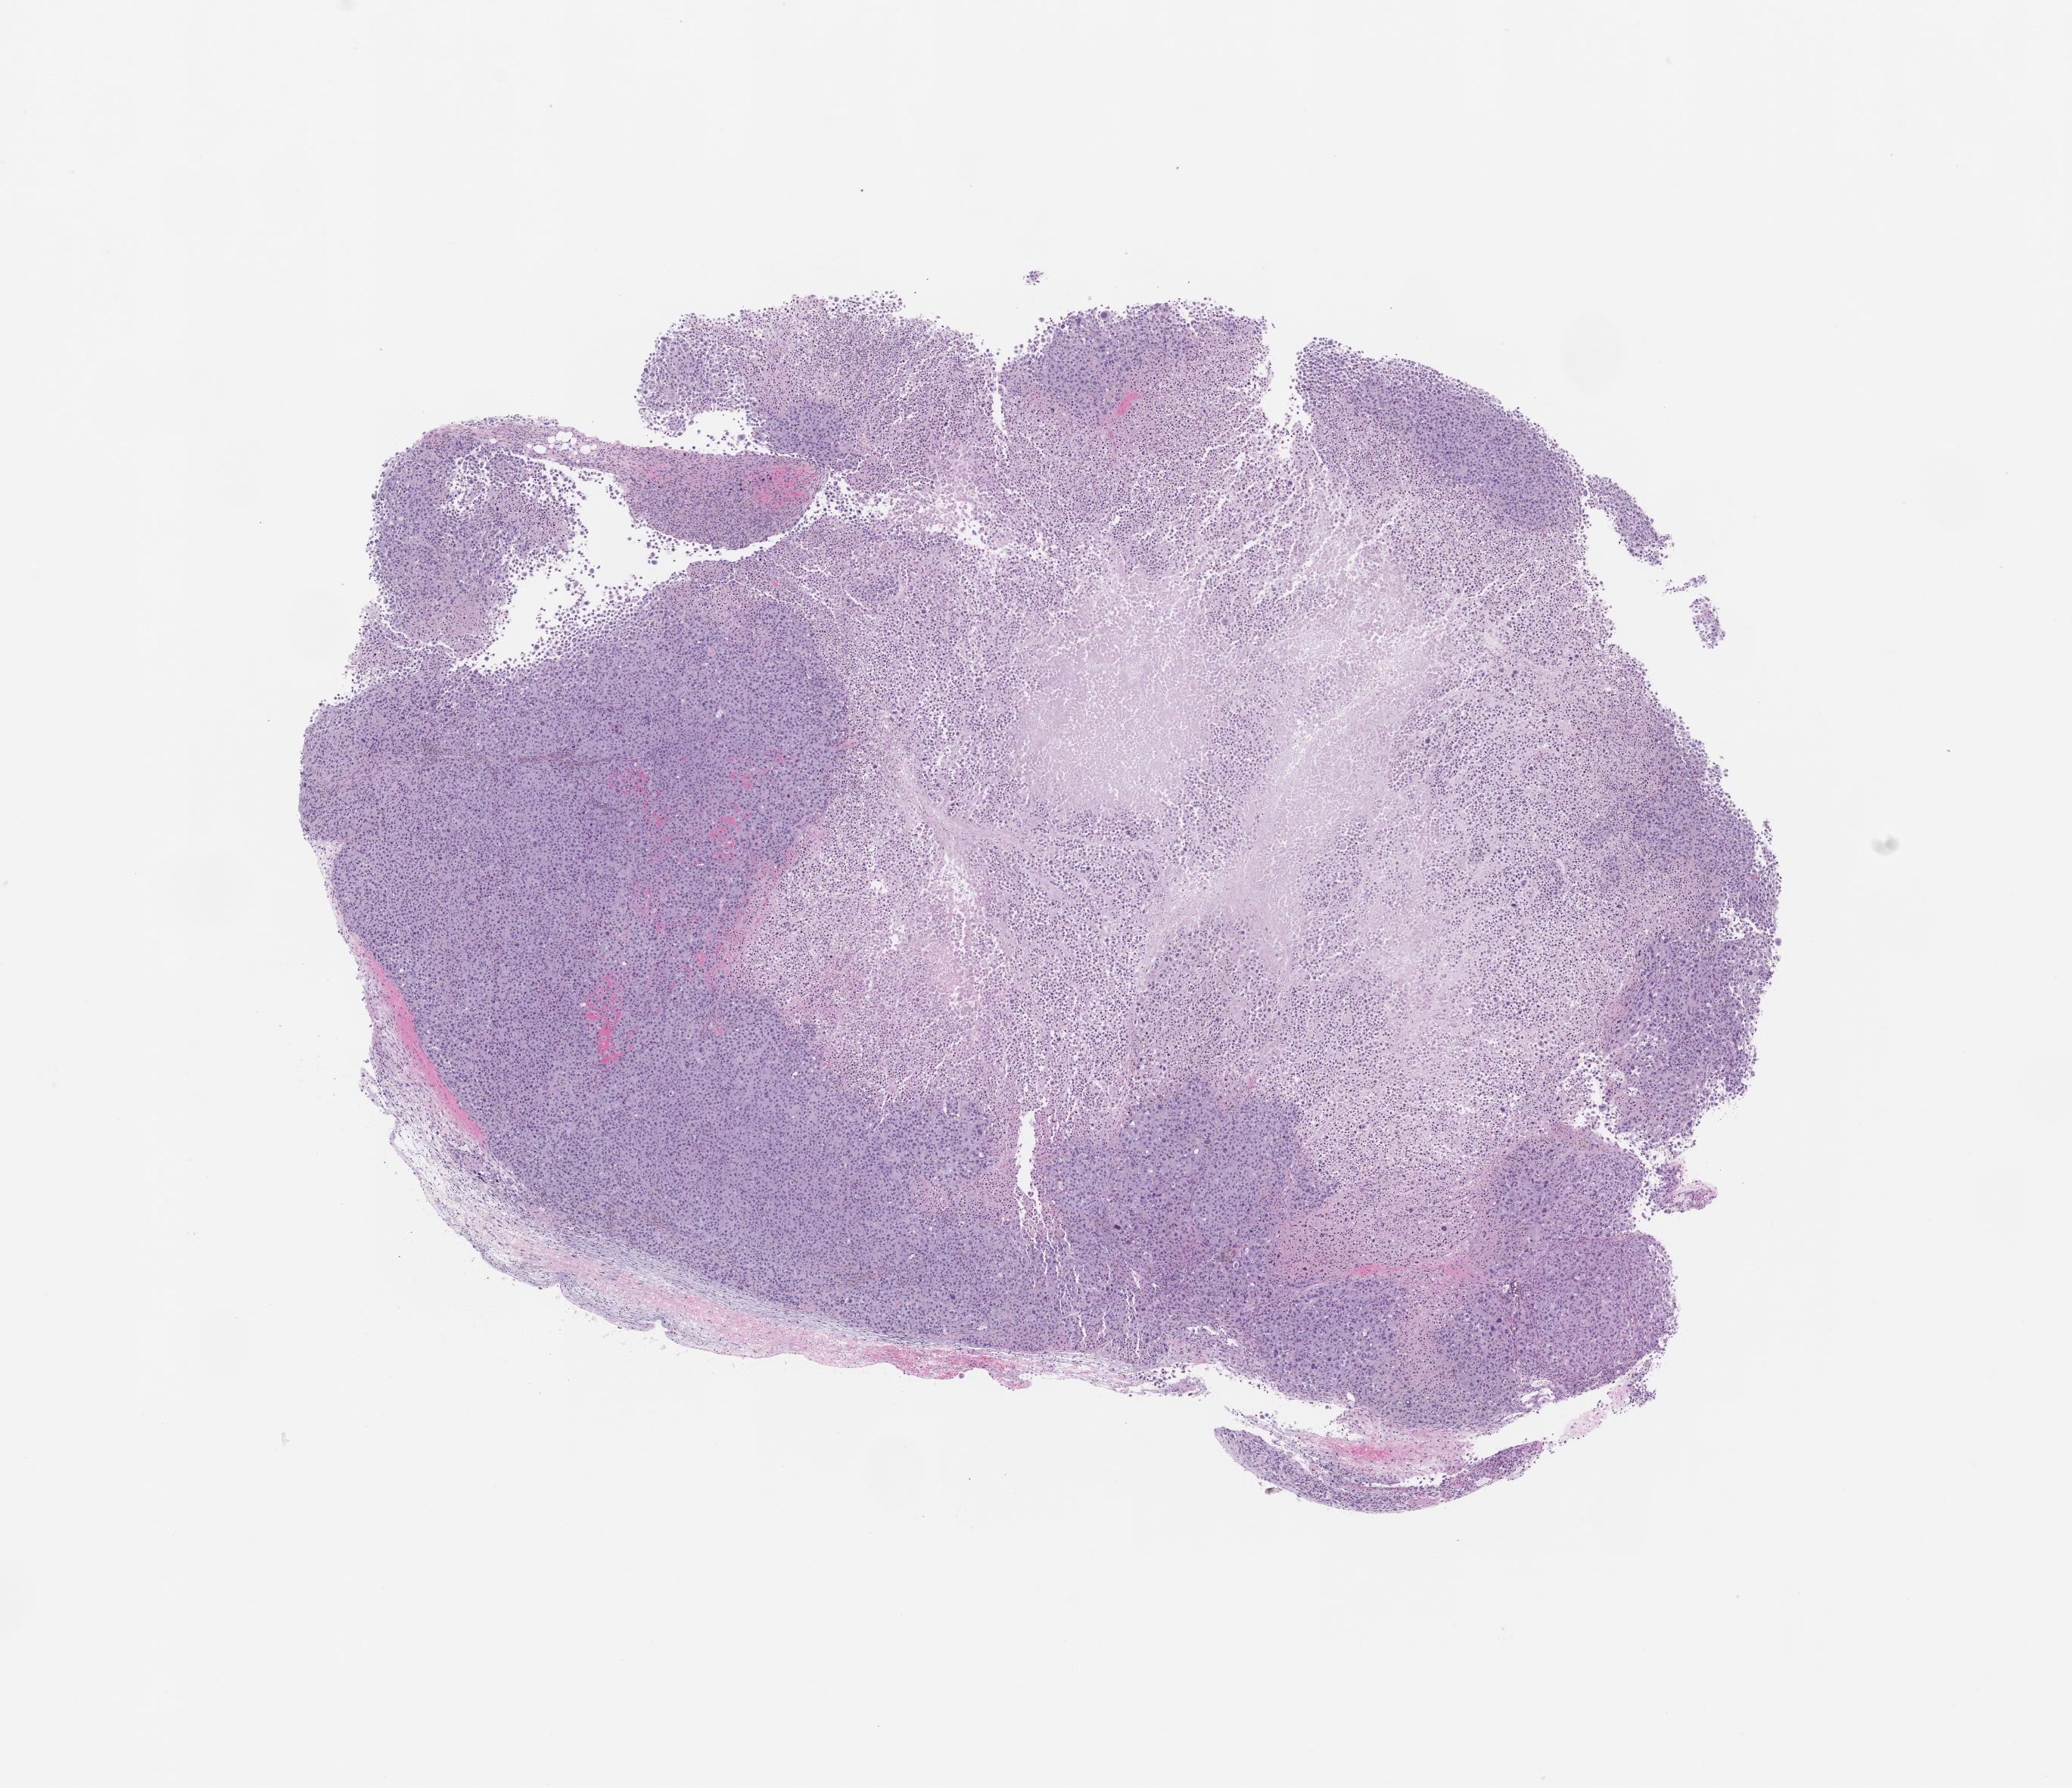
Whole-slide image, H&E: patient-derived xenograft (human tumor grown in a mouse), passage 0, whole scanned area (about 11.0 x 9.5 mm) shown as a low-resolution overview; FFPE section; originating tumor site category: skin.
- originating patient diagnosis: Melanoma